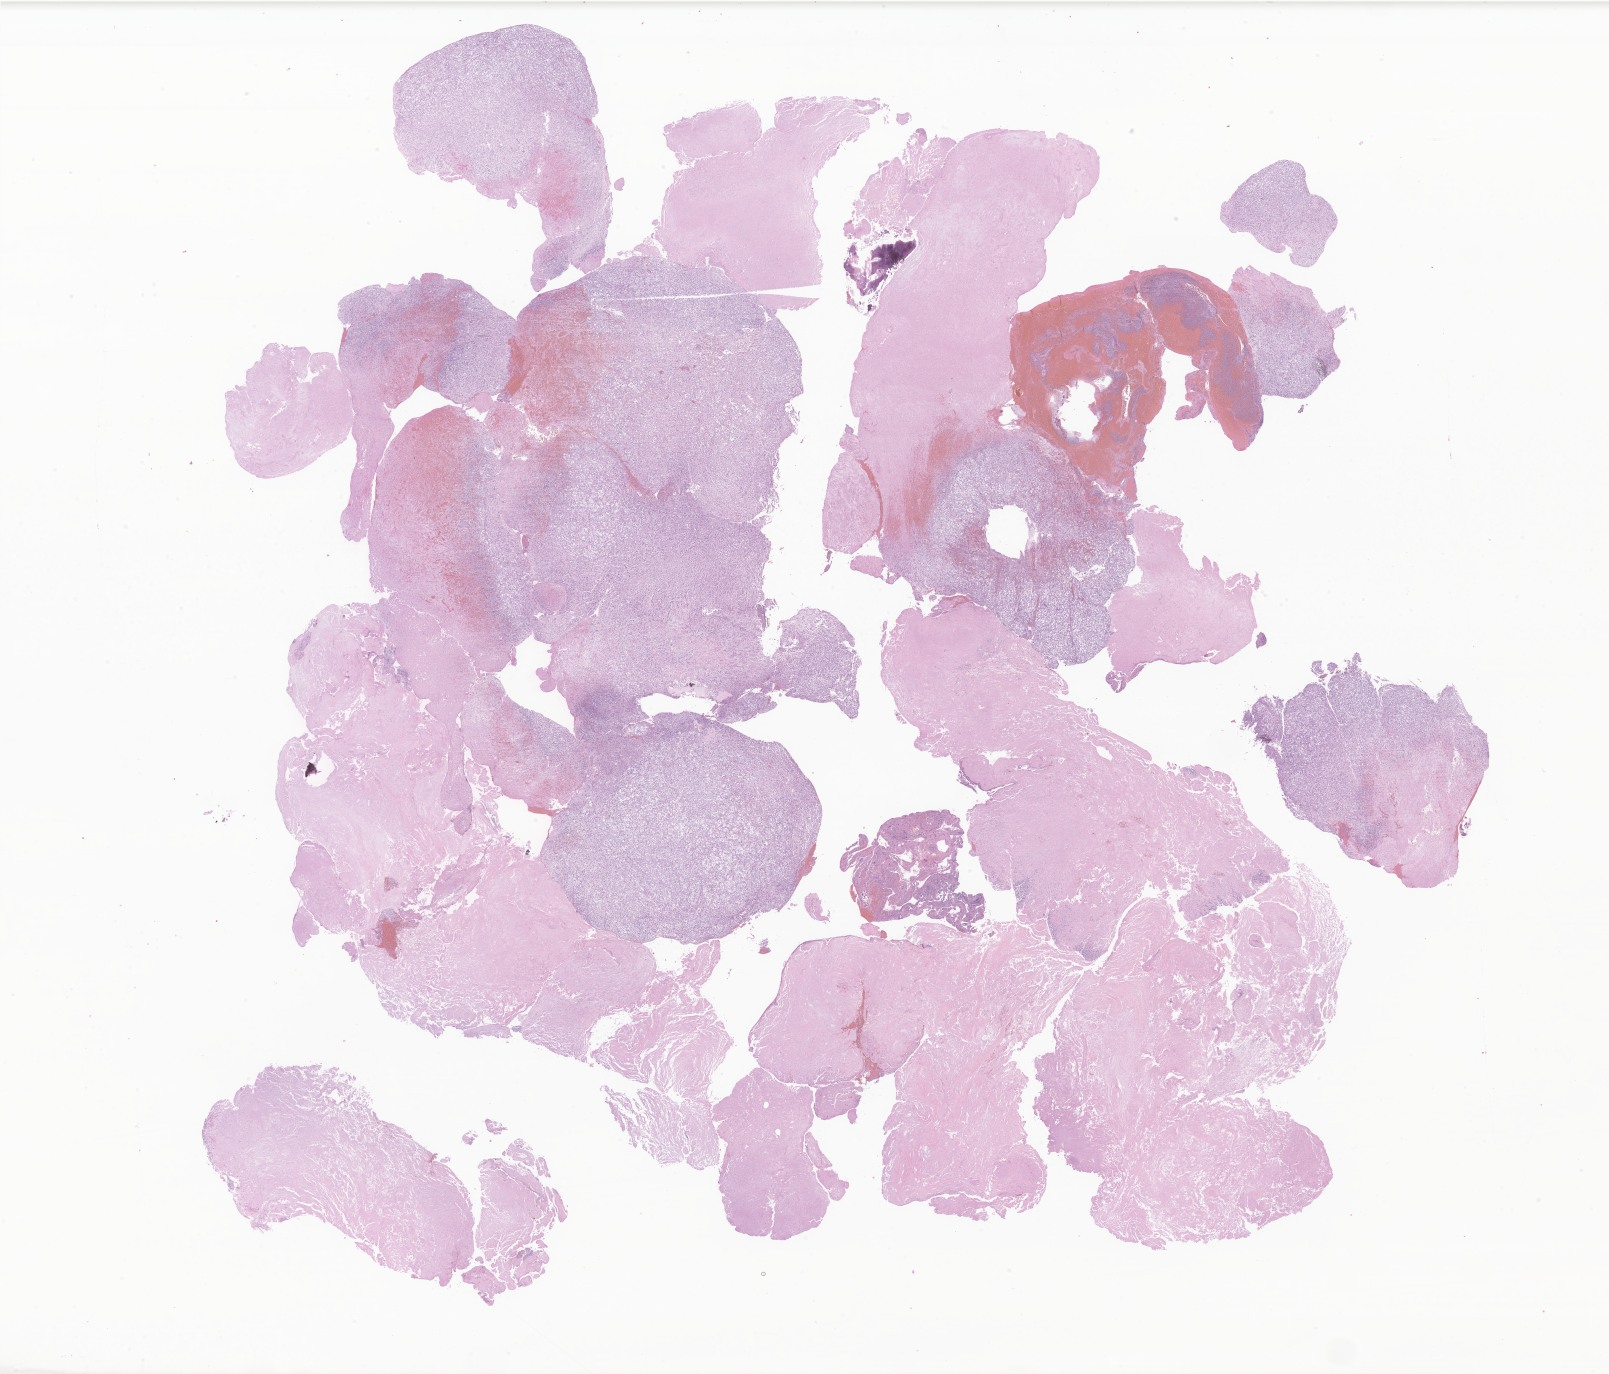
H&E whole-slide image of tumor tissue from the brain, a low-resolution overview of the entire scanned area, about 27.1 x 23.2 mm; formalin-fixed paraffin-embedded section. Patient: female, age 46 months (3 years 10 months).
Recorded diagnosis: Chordoma, NOS.